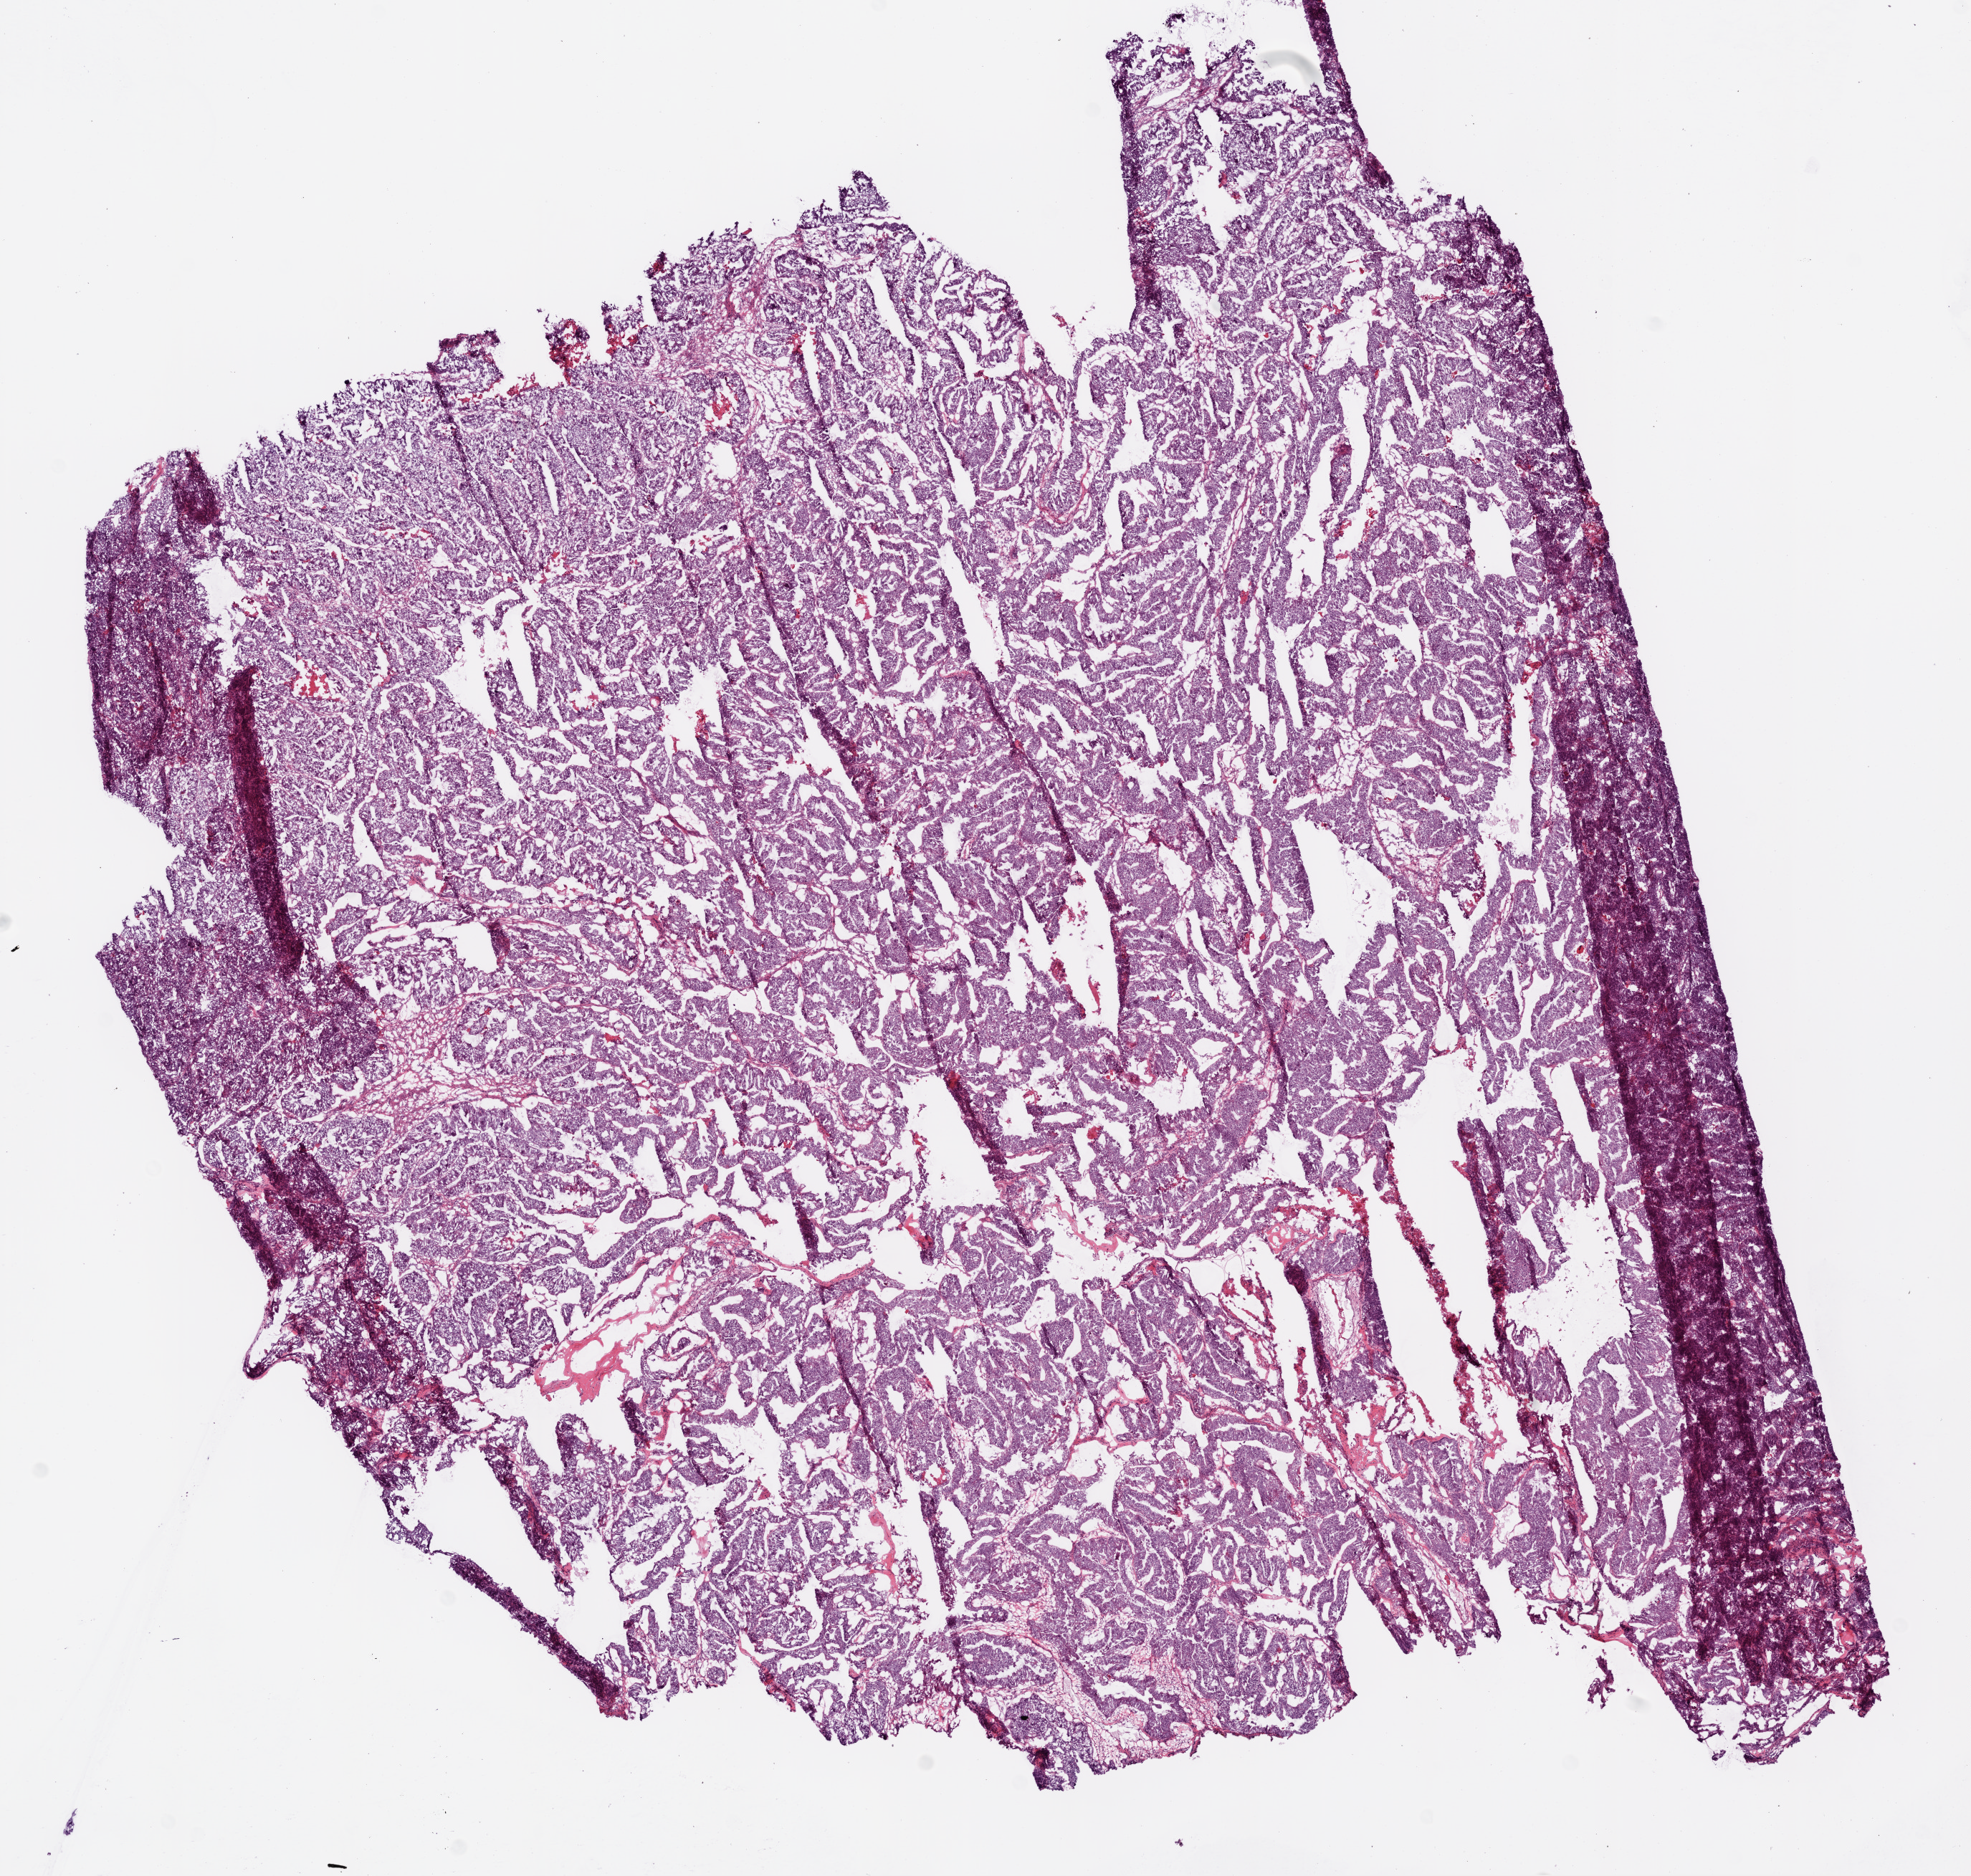
Digitized Hematoxylin and eosin (H&E) stained tissue section (whole slide) — shown as a low-resolution overview of the whole scanned area (about 11.0 x 10.5 mm, from a 20x scan), frozen section from the bottom of the tissue portion, sample: primary tumour, ovary. Female patient; age at initial diagnosis 51 years. Histologic grade: G4 (undifferentiated). Composition of this section per pathologist review: tumour cells 98%, tumour nuclei 95%, normal cells 0%, stromal cells 2%, necrosis 0%.
Histologic diagnosis: Serous cystadenocarcinoma, NOS. Laterality: left. FIGO stage: IIIC.